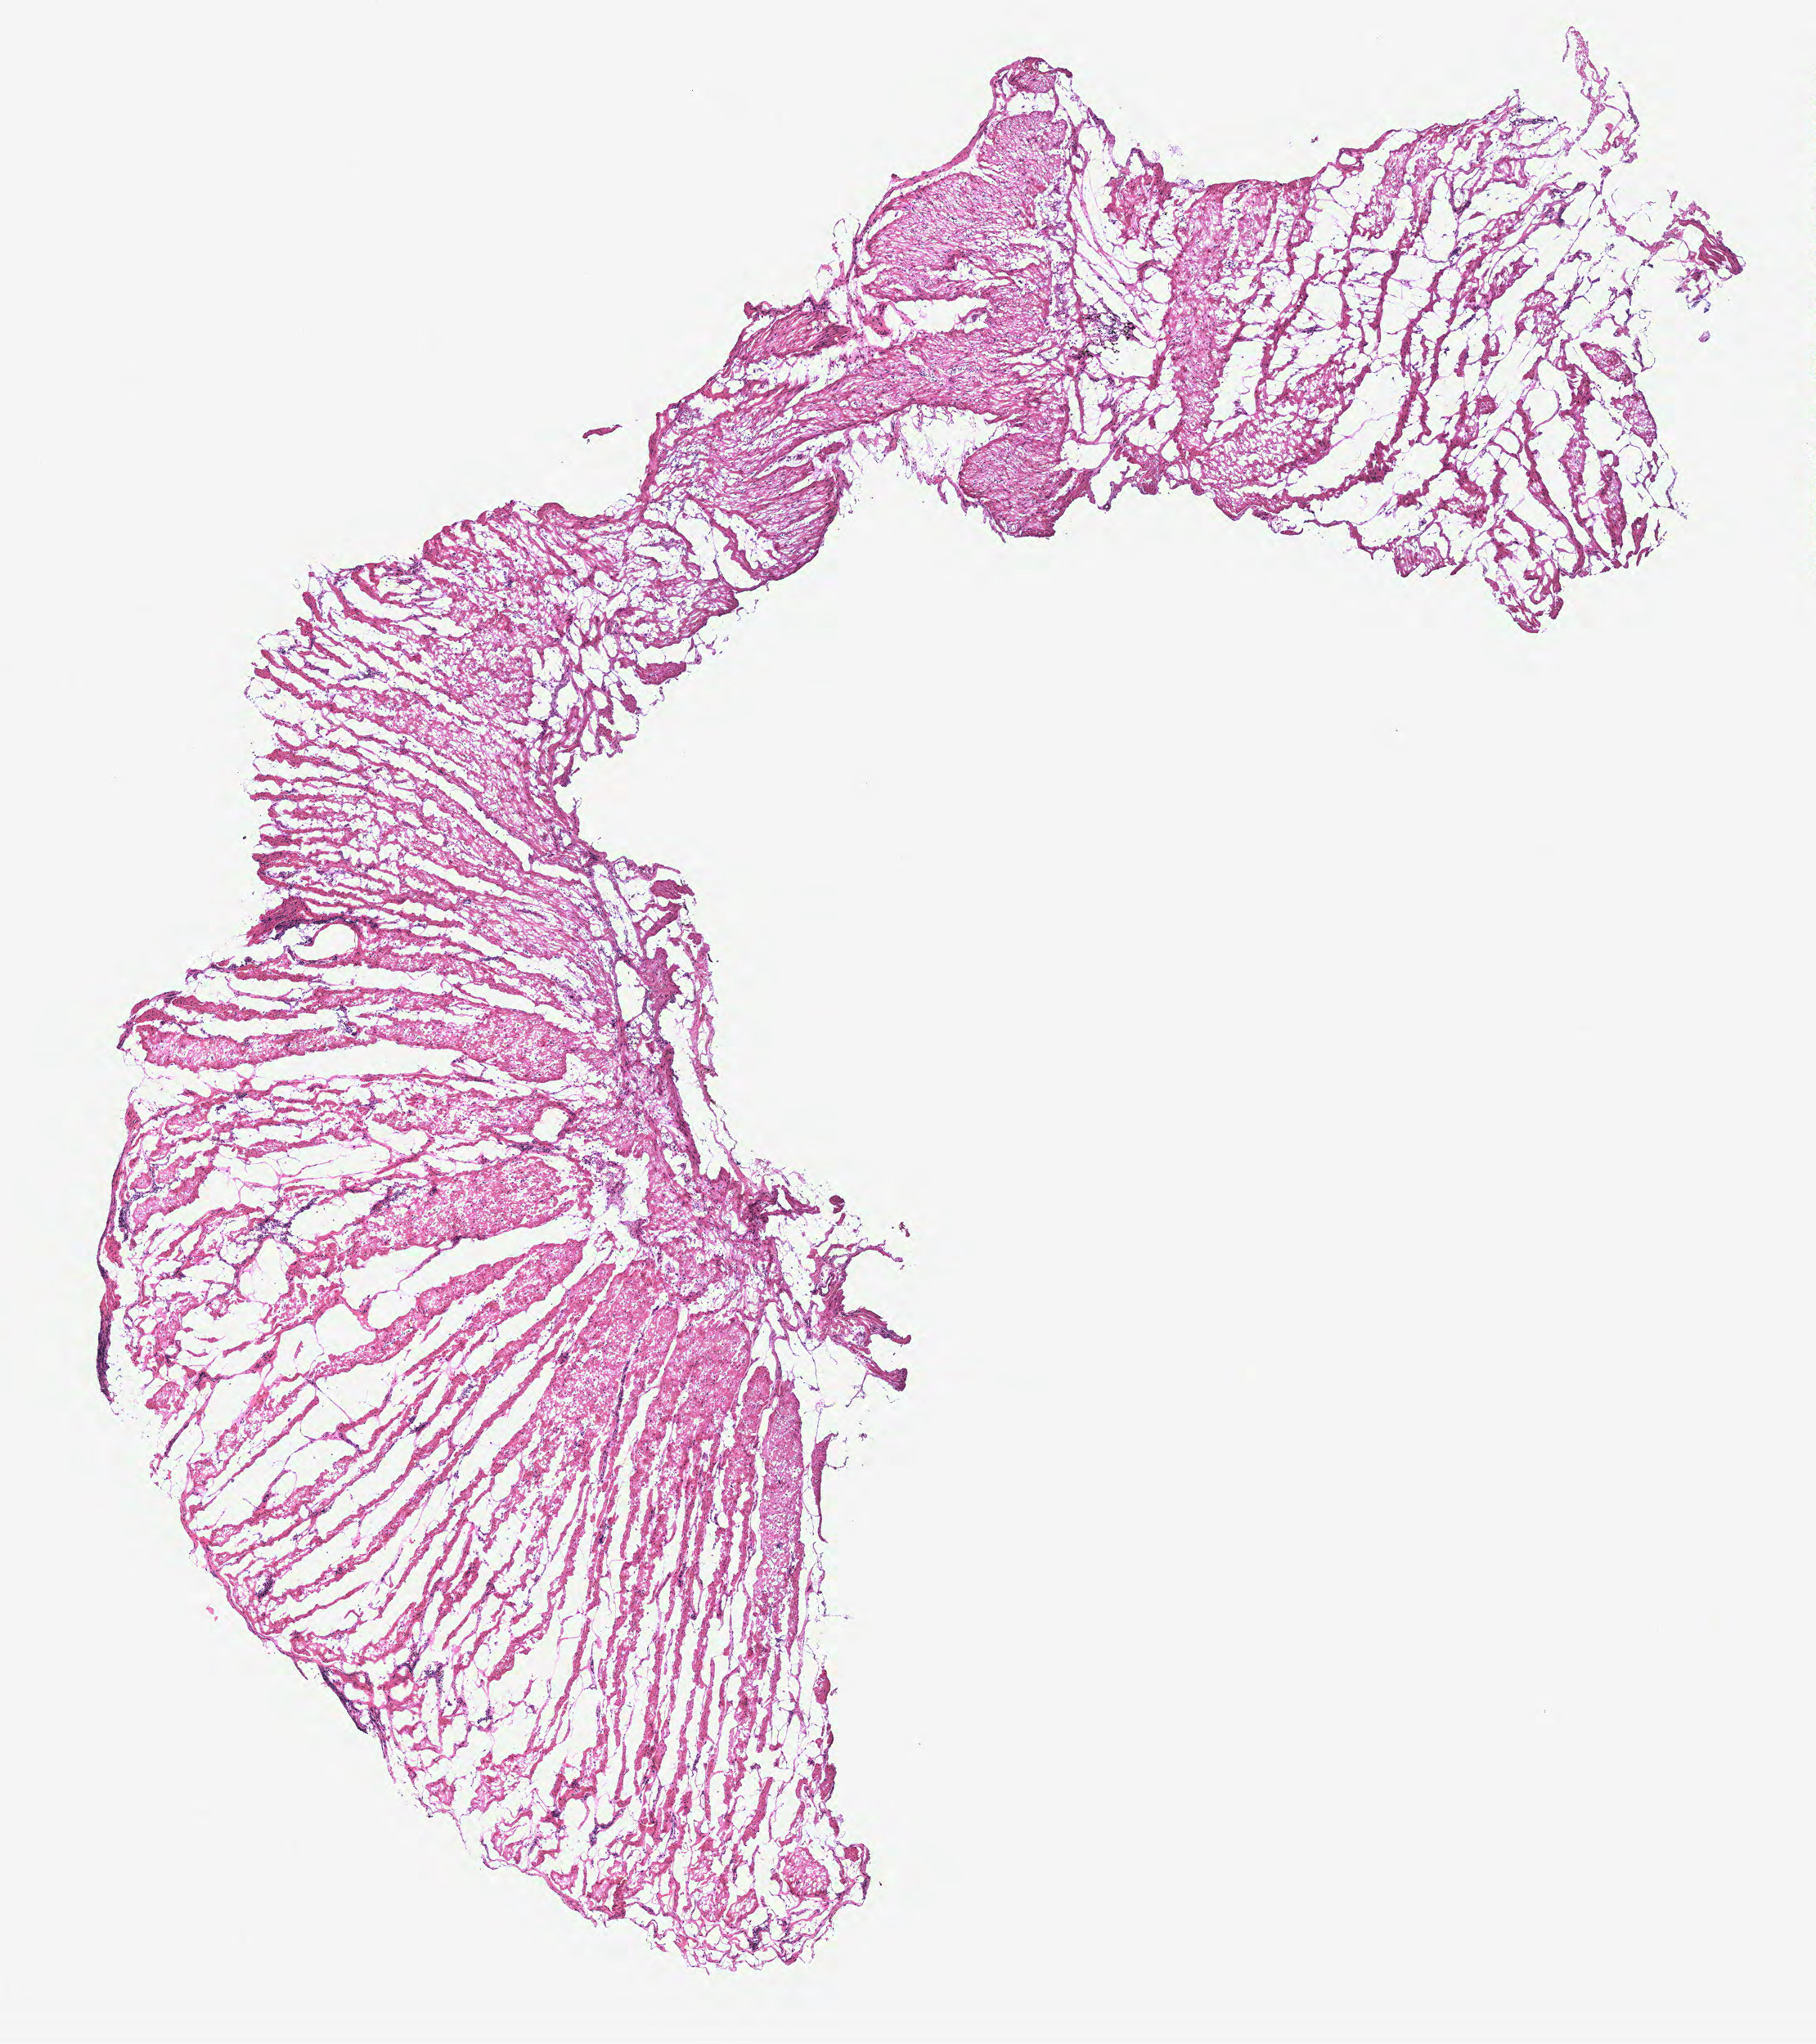
Whole-slide histology image, Hematoxylin and eosin (H&E) stained, shown as a low-resolution overview of the whole scanned area (about 8.9 x 10.0 mm); colon, tissue type not recorded.
Patient diagnosis (cohort enrolment): colon cancer (colon).